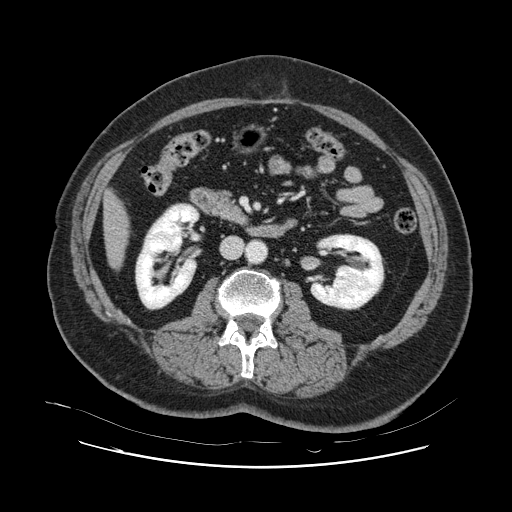
Contrast-enhanced abdominal CT, one axial slice. Intravenous contrast given. Soft-tissue window (W 400 / L 40 HU). 2.5 mm slice thickness. 512 × 512 image matrix. Female patient, age 73 years. From the clinical record (not read from this slice): diagnosis: colorectal cancer liver metastases, imaged before liver resection; multiple liver metastases: no; largest metastasis: 7 cm; chemotherapy before resection: yes.
Structures marked on this image (manually delineated by an expert):
- liver: bounding box <104,194,128,267> (left, top, right, bottom; pixels)
- planned liver remnant (the part of the liver to remain after resection): <105,194,128,266>